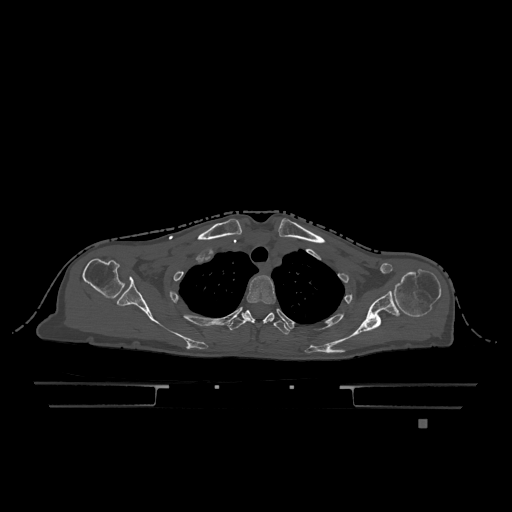
CT including the spine, one axial slice; position 945 of 1317 along the scan axis; bone window (W 1800 / L 400 HU); 512 × 512 image matrix, field of view 500 × 500 mm. Female patient, age 74 years. From the clinical record (not read from this slice): primary cancer: lung; vertebrae with lytic lesions (as recorded): T1, T4, T5, T6, L4, L5.
Outlined on this slice (semi-automatic segmentation, software-assisted and operator-edited):
- T2 vertebra: bounding box [x1, y1, x2, y2] px = [246, 275, 276, 304]
- T3 vertebra: [228, 310, 290, 335]
- T6 vertebra: [267, 313, 274, 318]